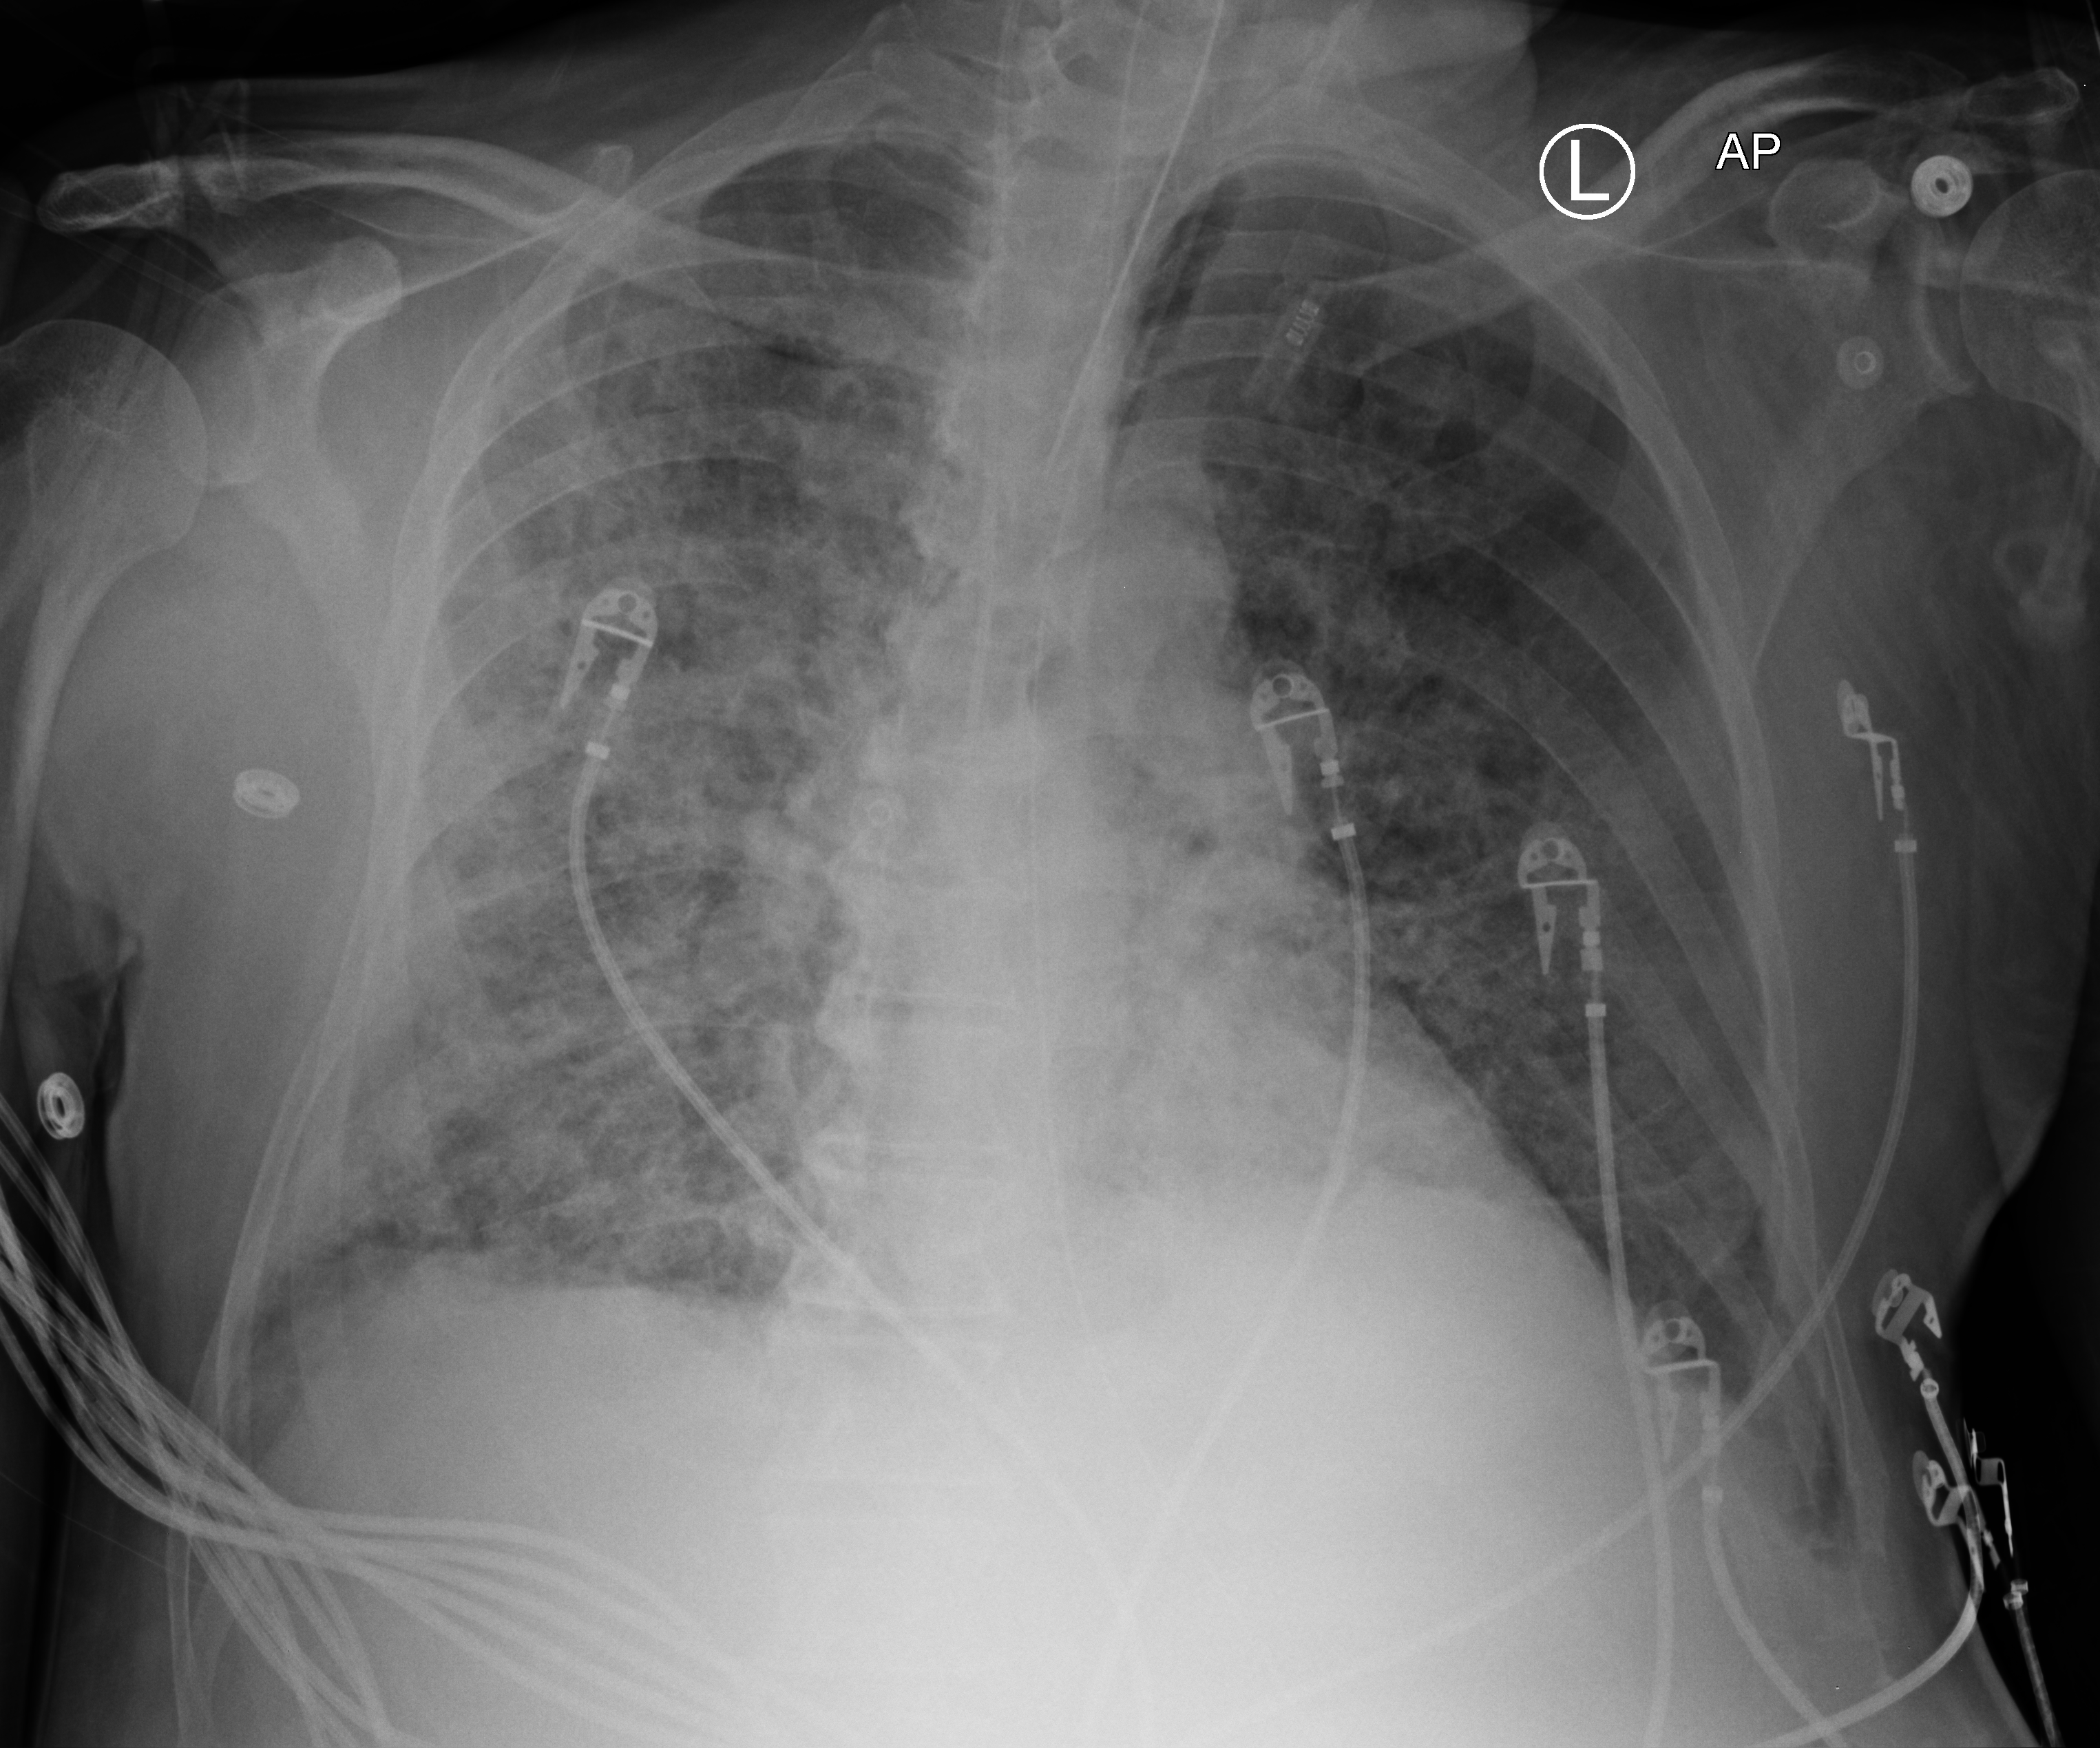
Chest X-ray (portable). Patient hospitalised with COVID-19; male, aged 60–74 years.
From the hospital-stay record, not from the radiograph (when in the stay this image was taken is not recorded): smoking status (admission record): never.